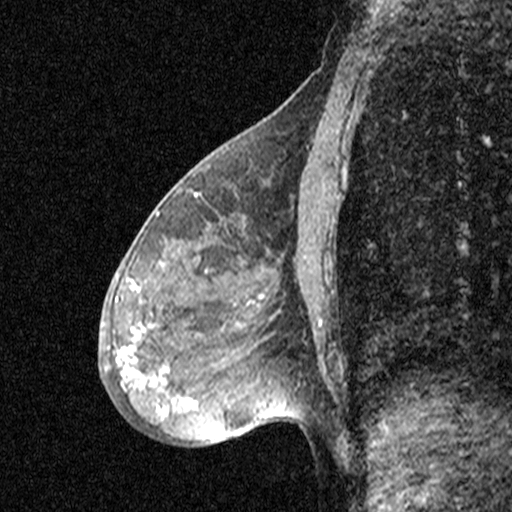
Breast MRI (dynamic contrast-enhanced), one sagittal slice. Slice 20 of 44 in the series (ordered by position). Dynamic contrast-enhanced study with each time point stored as its own series, time point 2 of 3 at this slice position (early post-contrast, ordered by acquisition time). 1.5 T. TE 4.5 ms, TR 11 ms. 3 mm slice thickness. 512 × 512 image matrix. Patient: female, 53 years. Case-level facts recorded for this patient, not image findings: setting: breast cancer imaged before/during neoadjuvant chemotherapy; receptor status: HR-positive, HER2-negative.
Structures marked on this image (semi-automatic segmentation, software-assisted and operator-edited):
- analysis volume of interest (the breast-tissue region the enhancement analysis was run in; not a lesion): bounding box [x1, y1, x2, y2] px = [88, 176, 313, 423]
- tumour enhancement mask (voxels above the 90 % enhancement threshold inside the analysis volume of interest): [117, 284, 190, 411]